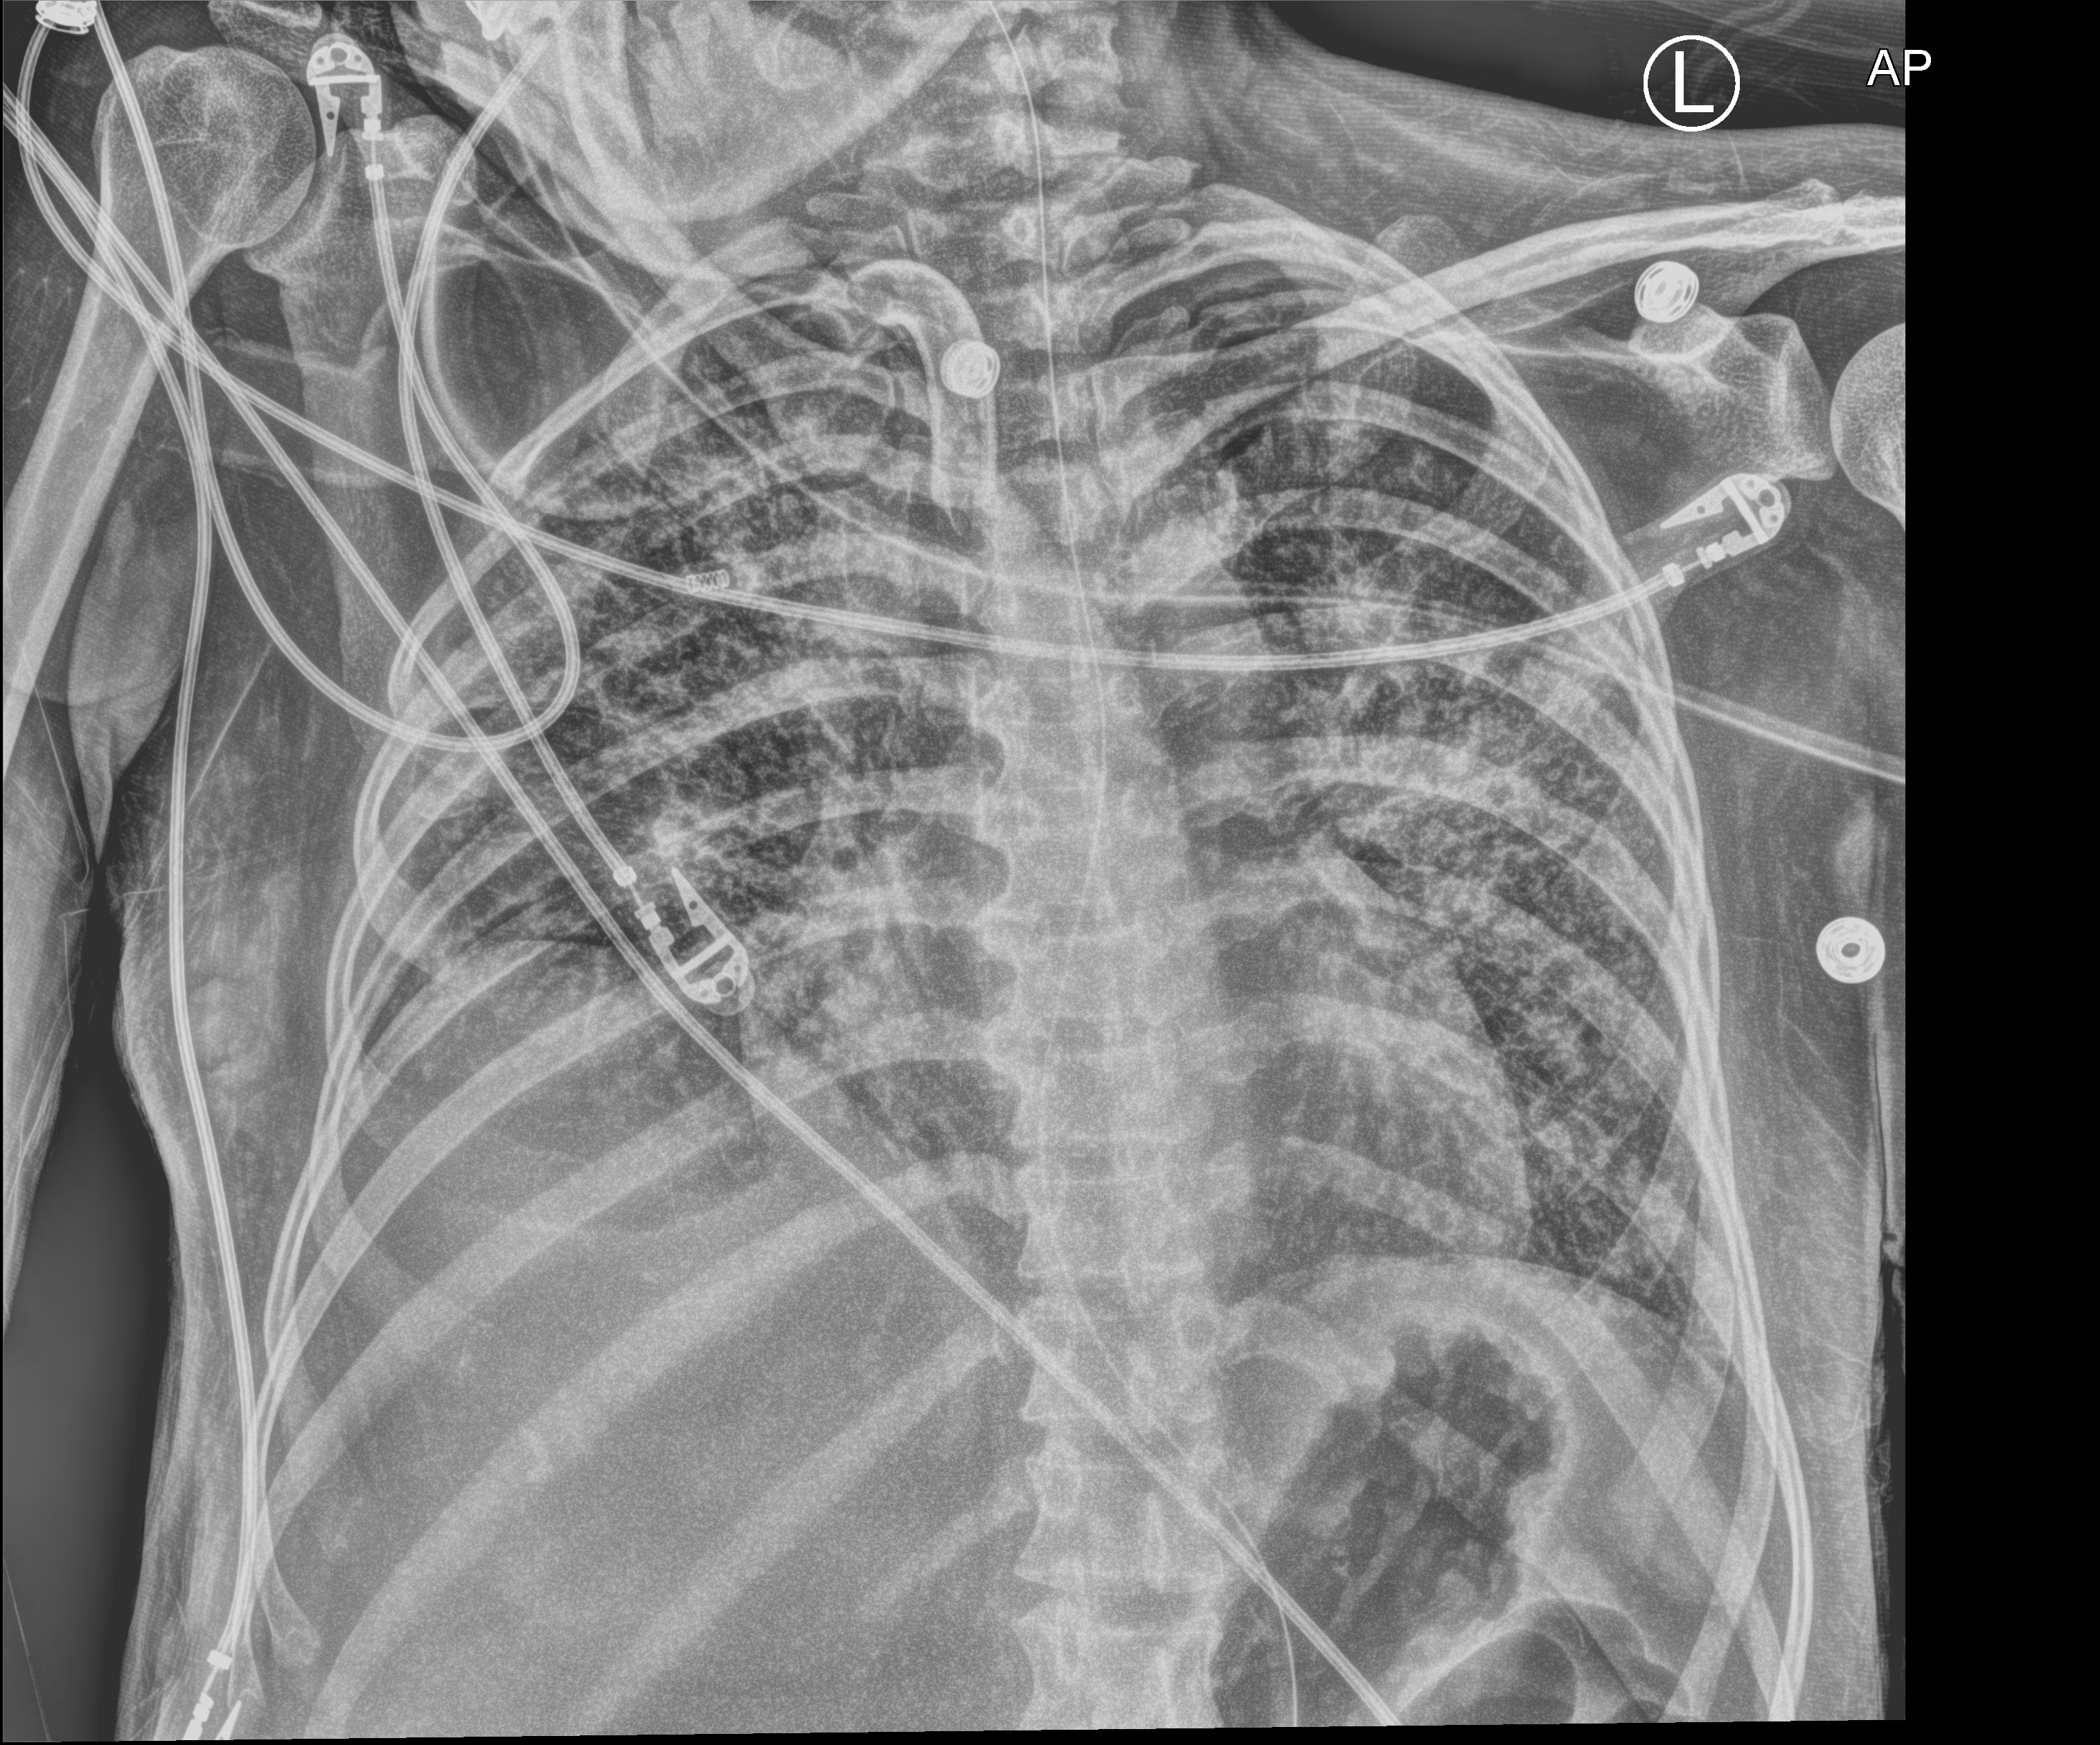
Chest X-ray (portable); anteroposterior (AP) projection. Patient hospitalised with COVID-19; female, aged 18–59 years.
Admission-level facts for this patient (not findings on this image; timing relative to this image not recorded): admitted to intensive care during this hospital stay: yes.